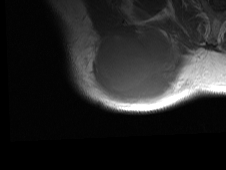
MRI of an extremity soft-tissue mass, one axial slice; slice 55 of 81 in the series (ordered by position); MR volume resampled by the dataset authors to the PET/CT grid (not the native acquisition matrix); 3.27 mm slice thickness; 226 × 170 image matrix, field of view 221 × 166 mm. Male patient. Case-level facts recorded for this patient, not image findings: histological type: pleiomorphic spindle cell undifferentiated; grade: high; site of the primary tumour: right parascapusular.
Structures marked on this image (expert contour drawn on MRI and transferred to this co-registered scan by the dataset authors):
- gross tumour volume including surrounding oedema: bounding box (x1, y1, x2, y2) in pixels: (85, 27, 196, 107)
- gross tumour volume (mass): (94, 33, 173, 105)